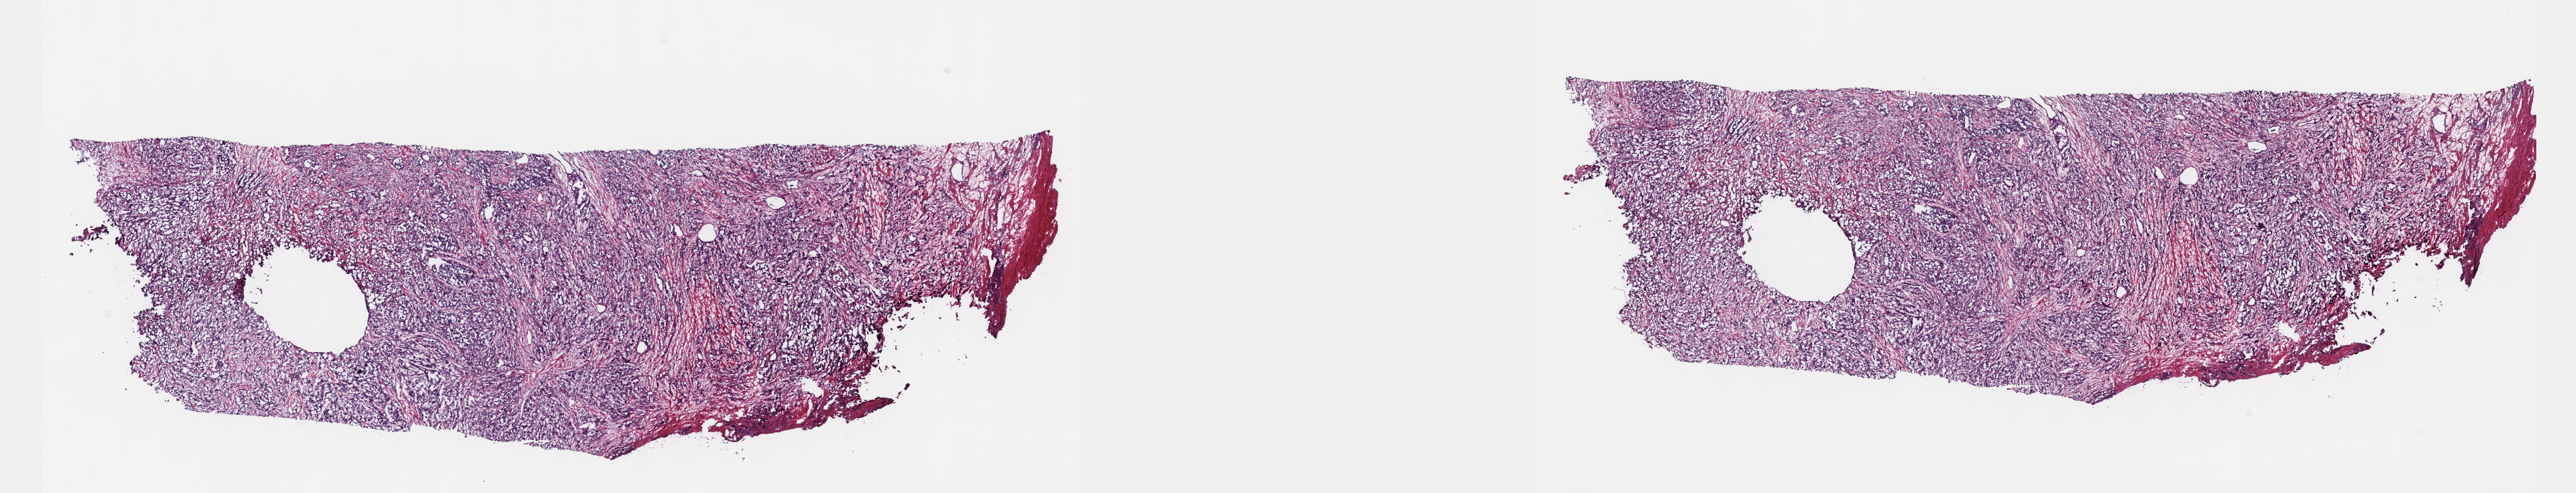
H&E whole-slide image, low-resolution overview of the scanned area, about 31.2 x 6.0 mm (acquisition: 40x scan), frozen section from the top of the tissue portion, prostate, primary tumour sample. Male, age 58 years at initial diagnosis. Gleason score: 9 (5+4). Pathologist review of this section (percent, as recorded): tumour cells 70%, tumour nuclei 80%, normal cells 0%, stromal cells 30%, necrosis 0%. Infiltration values recorded for this section: lymphocyte infiltration 0%, monocyte infiltration 0%, neutrophil infiltration 0%.
Lymph nodes positive (case pathology): 1 of 3 examined. Laterality: bilateral. Diagnosis: Adenocarcinoma, NOS (prostate gland).